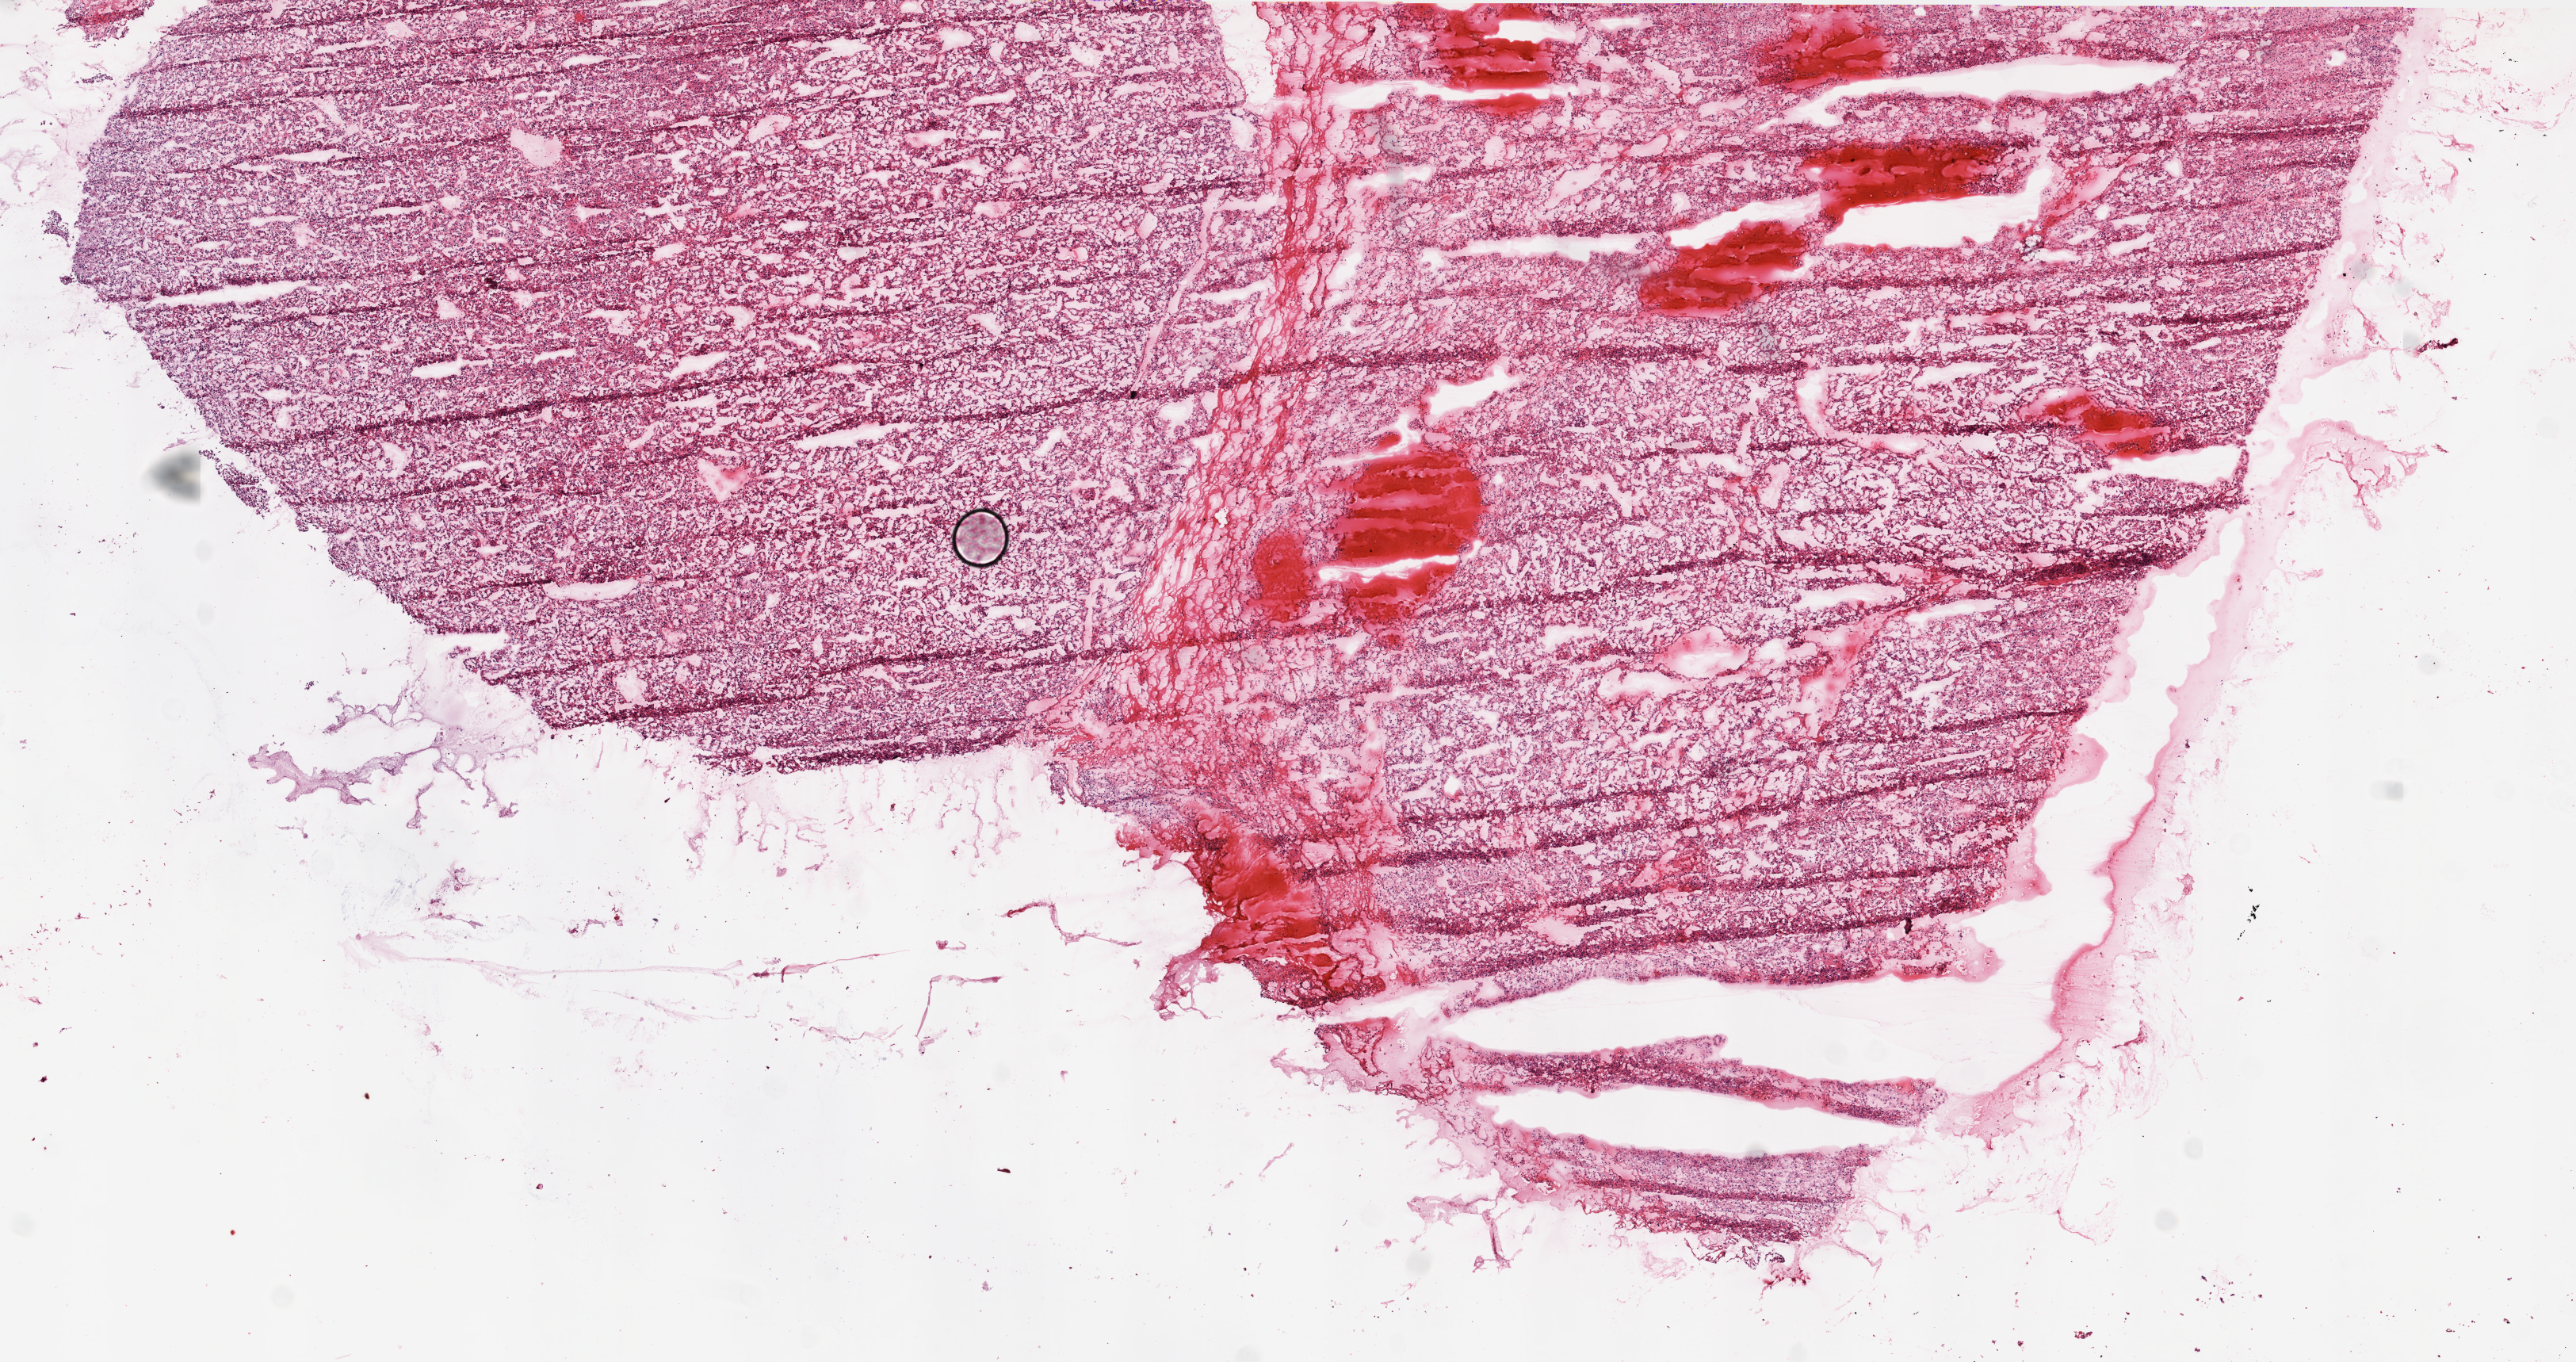
Whole-slide histology image, Hematoxylin and eosin (H&E) stained, a low-resolution overview of the entire scanned area, about 13.0 x 6.9 mm, frozen section, kidney, primary tumour sample. Patient: female, age at initial diagnosis 82 years. Histologic grade: G2 (moderately differentiated). Slide review estimates, as recorded: tumour cells 95%, tumour nuclei 90%, normal cells 0%, stromal cells 5%, necrosis 0%.
• AJCC pathologic stage: I
• pathologic diagnosis: Clear cell adenocarcinoma, NOS